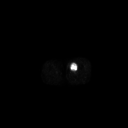
FDG PET of an extremity soft-tissue mass (from a PET/CT study), one axial slice; slice 221 of 267 in the series (ordered by position); 3.27 mm slice thickness; 128 × 128 image matrix. Patient: male, 48 years. From the clinical record (not read from this slice): histological type: pleiomorphic leiomyosarcoma; grade: high; site of the primary tumour: left thigh.
Outlined on this slice (expert contour drawn on MRI and transferred to this co-registered scan by the dataset authors):
- gross tumour volume including surrounding oedema: bounding box (x1, y1, x2, y2) in pixels: (69, 62, 78, 72)
- gross tumour volume (mass): (69, 62, 77, 72)